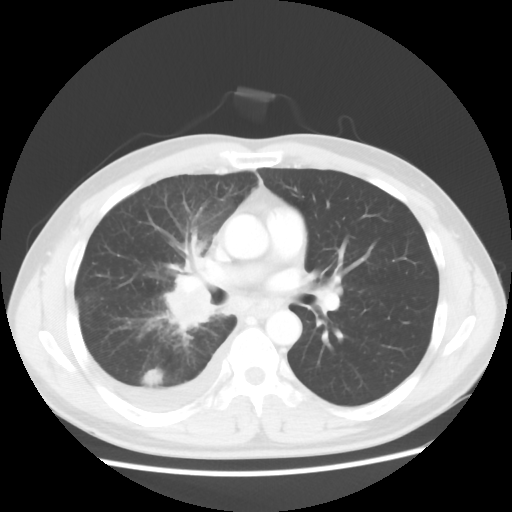
Chest CT, one axial slice; position 30 of 56 along the scan axis; reconstruction kernel STANDARD; 120 kVp; lung window (W 1500 / L -600 HU); 5 mm slice thickness; 512 × 512 image matrix. Male patient, age 46 years. Case-level facts recorded for this patient, not image findings: clinical TNM (as recorded): T2 N3 M1.
Annotated regions visible in this slice (rectangle marked by the reading radiologist):
- lung tumour (recorded histology: adenocarcinoma): bounding box (x1, y1, x2, y2) in pixels: (162, 268, 218, 332)